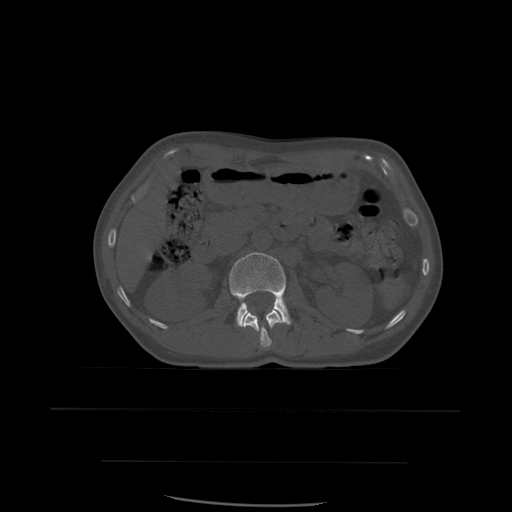
CT including the spine, one axial slice; position 235 of 574 along the scan axis; bone window (W 1800 / L 400 HU); 1.25 mm slice thickness; 512 × 512 image matrix, field of view 392 × 392 mm. Patient age 48 years. From the clinical record (not read from this slice): primary cancer: lung; vertebrae with lytic lesions (as recorded): T11.
Annotated regions visible in this slice (semi-automatically segmented with operator editing):
- L1 vertebra: bounding box [x1, y1, x2, y2] px = [242, 310, 284, 348]
- L2 vertebra: [229, 252, 291, 327]